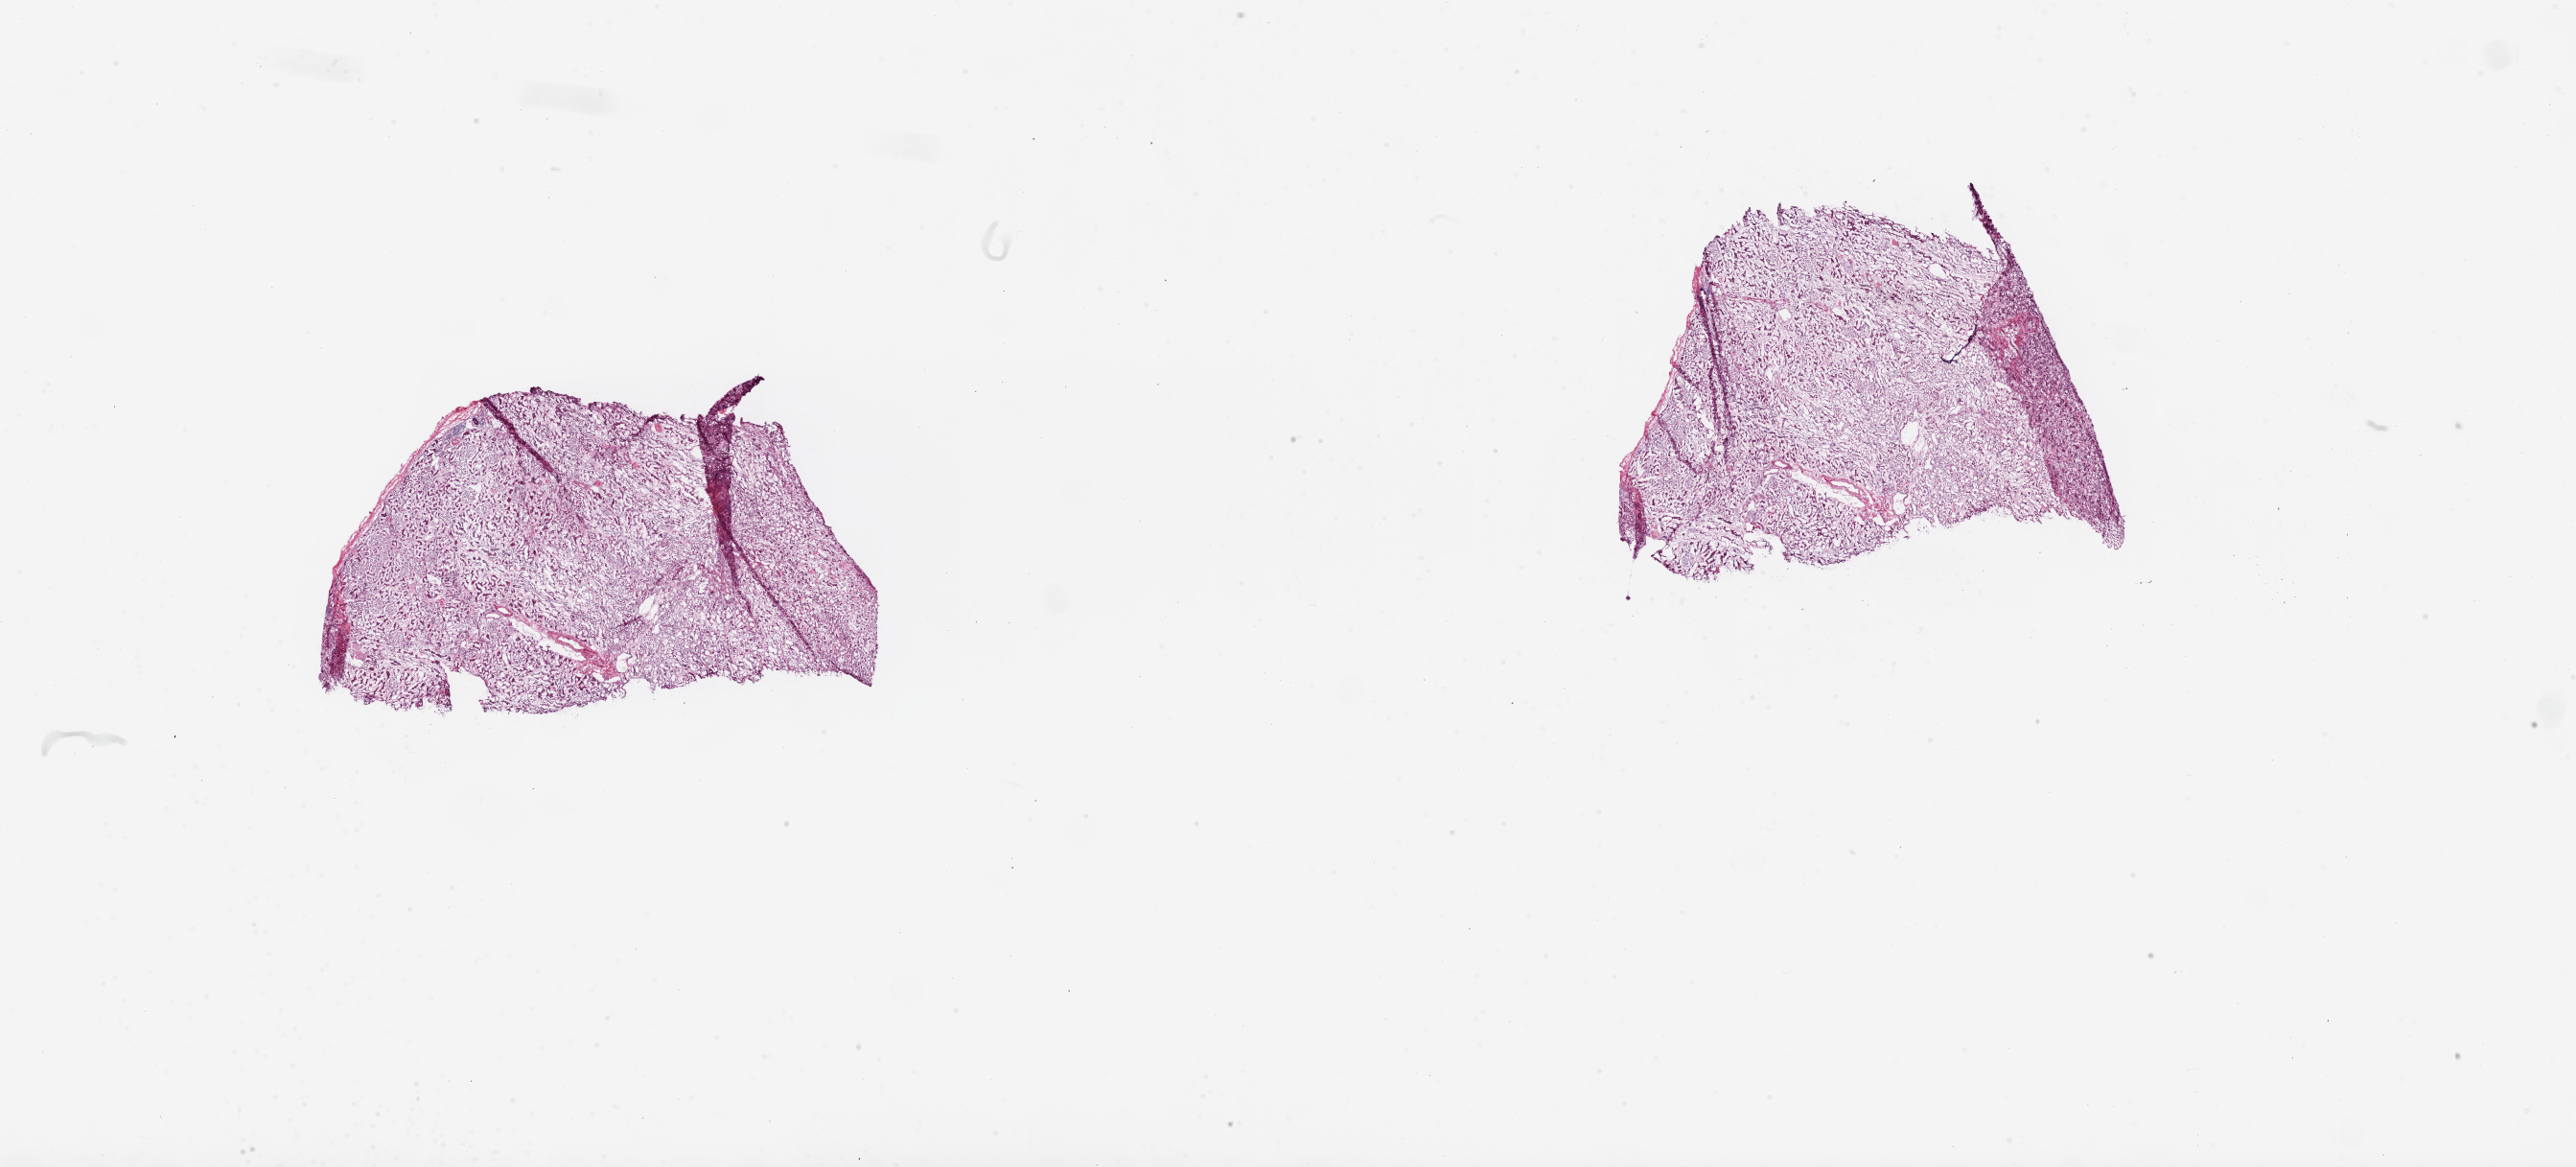
Hematoxylin and eosin (H&E) stained whole-slide image, low-resolution overview of the scanned area, about 43.1 x 19.5 mm. Frozen section. Kidney, solid tissue normal (non-tumour tissue) sample. Male patient; age at initial diagnosis 68 years.
This section: solid tissue normal (non-tumour) sample from the same patient. Patient diagnosis: Clear cell adenocarcinoma, NOS.